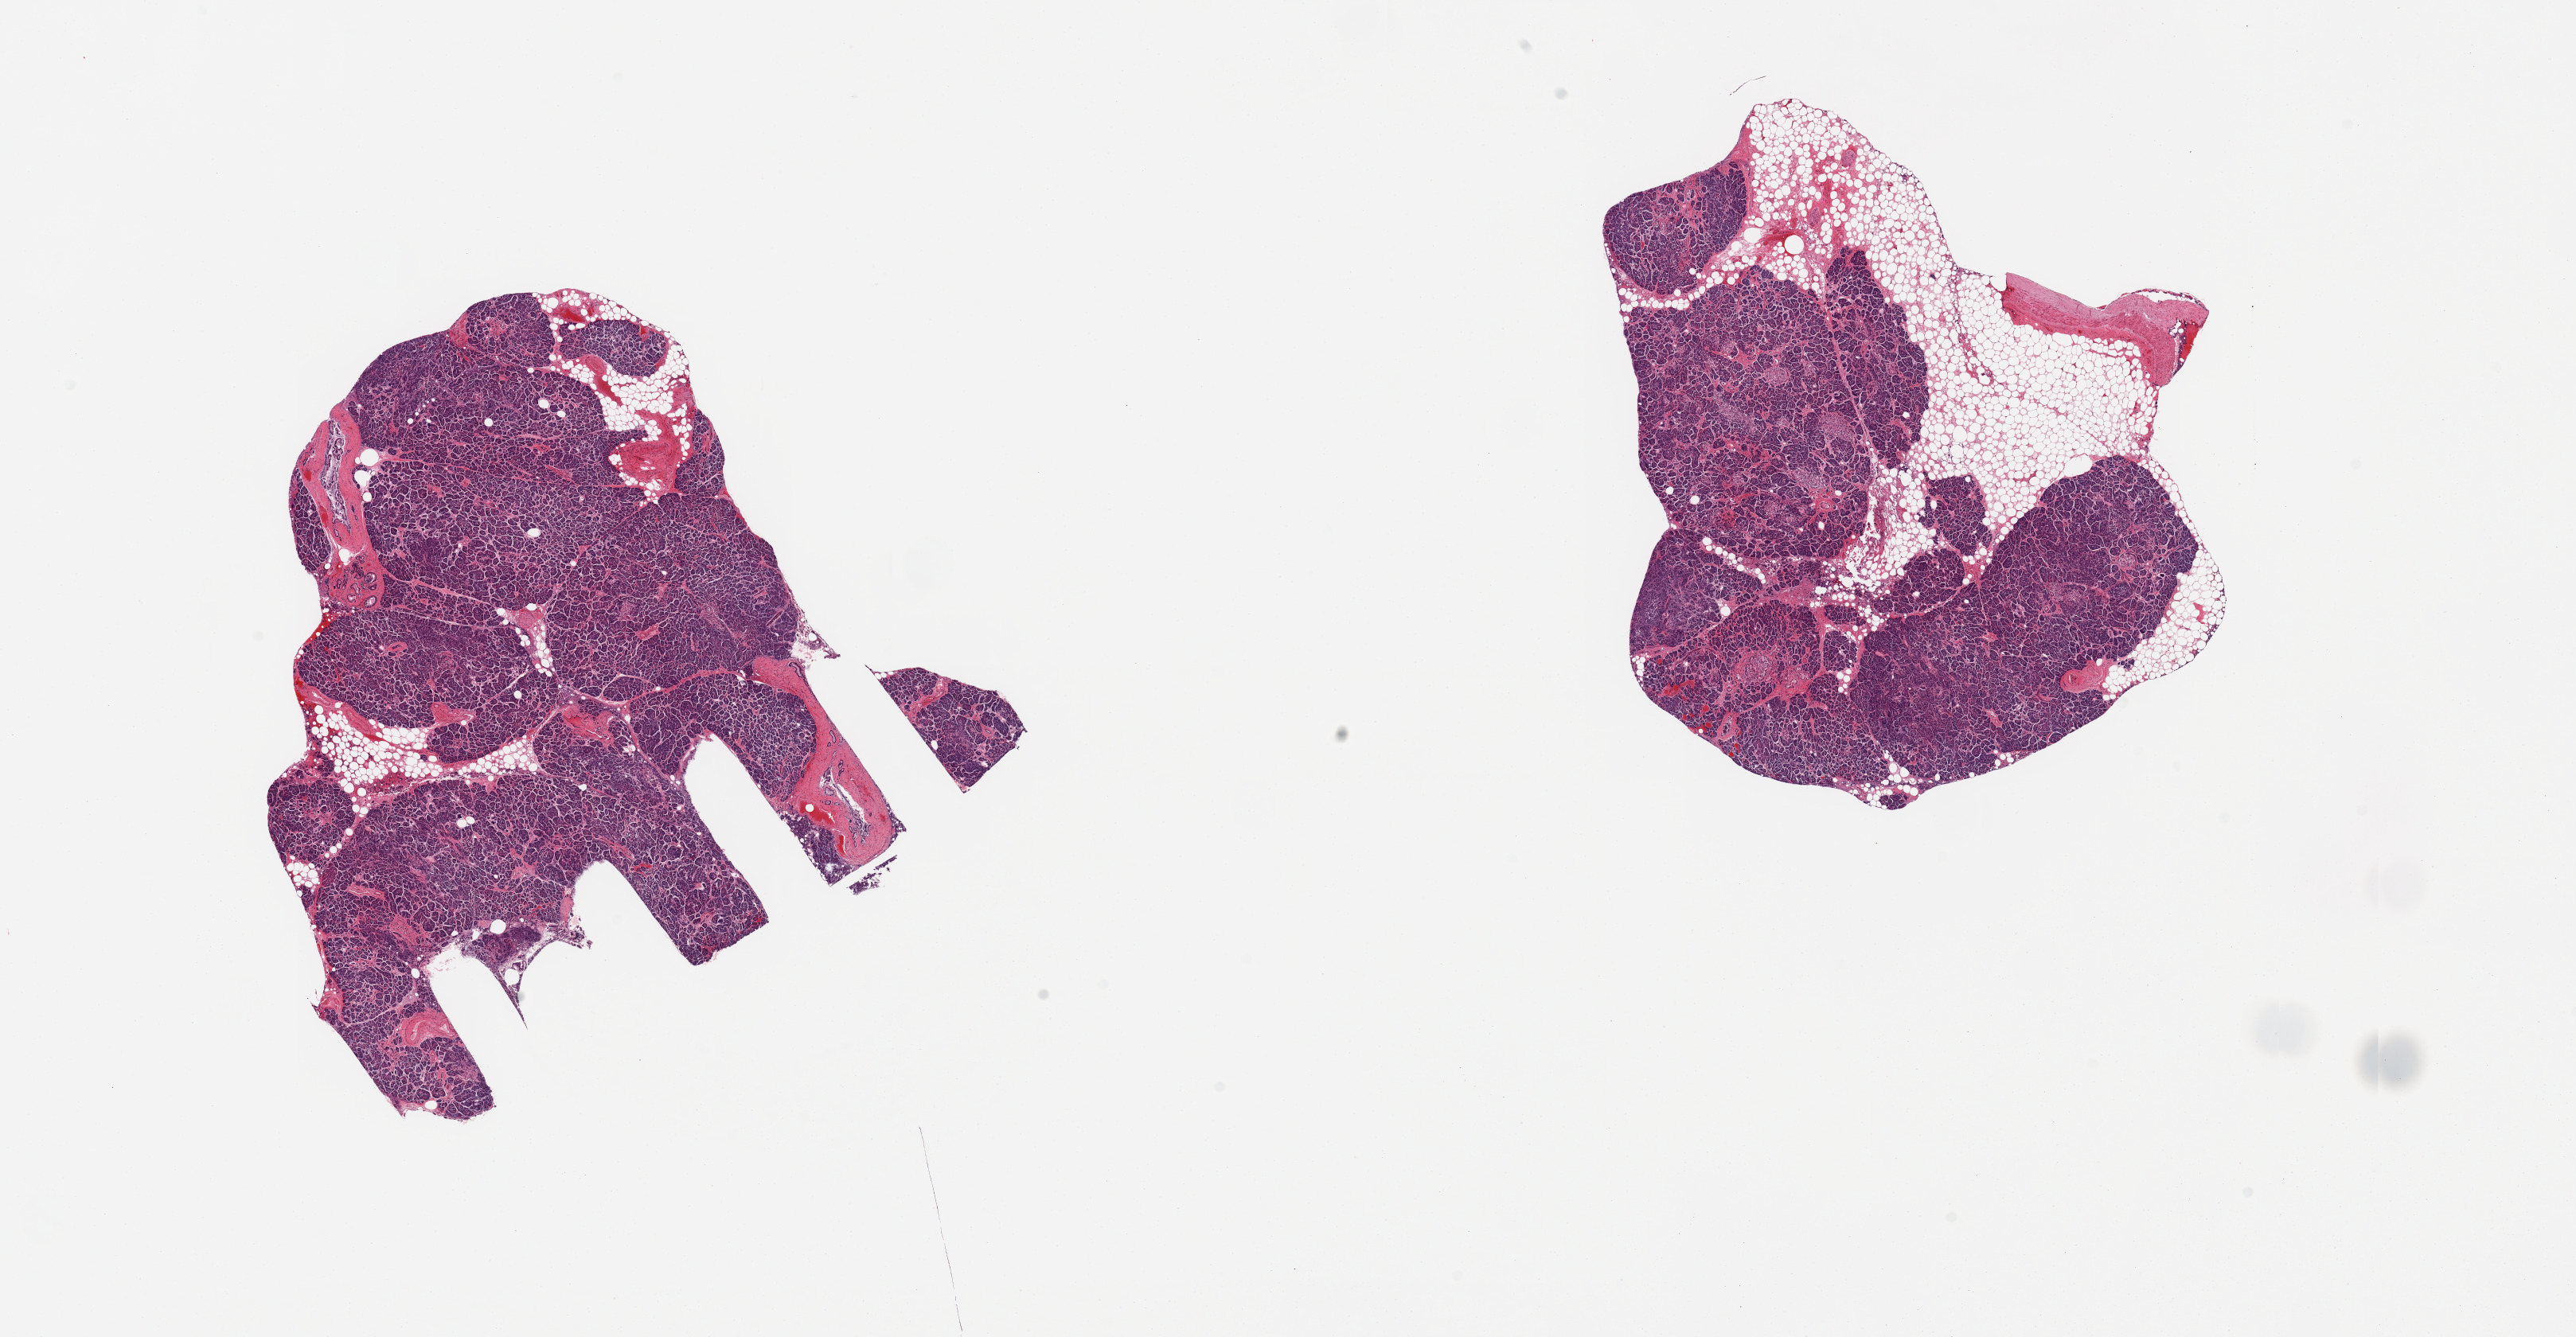
Digitized hematoxylin and eosin (H&E)-stained section — low-resolution overview of the scanned area, about 25.6 x 13.3 mm (from a 20x scan). PAXgene-fixed paraffin-embedded (PFPE) section. Section of pancreas (target tissue). Donor tissue sample. Donor: male.
Pathologist's review note for this sample: 2 pieces, ~30% adherent fat; An occsaional degenerating Islet is noted (one); moderately advanced autolysis/saponification.